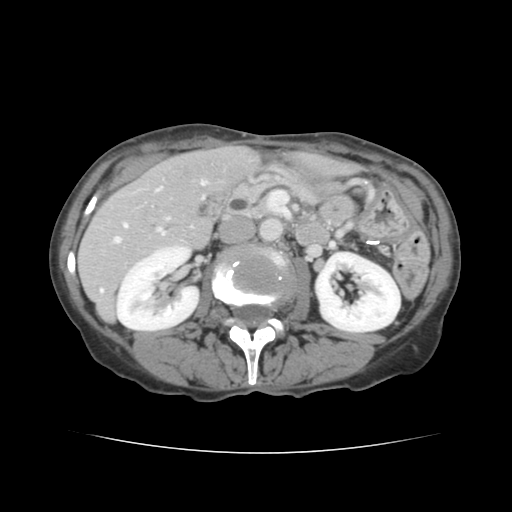
Contrast-enhanced abdominal CT, one axial slice; position 59 of 136 along the scan axis; intravenous contrast given; soft-tissue window (W 400 / L 40 HU); 2.5 mm slice thickness; 512 × 512 image matrix, field of view 319 × 319 mm. Female patient, age 77 years. Case-level facts recorded for this patient, not image findings: diagnosis: colorectal cancer liver metastases, imaged before liver resection.
Outlined on this slice (outlined manually by an expert reader):
- hepatic veins: bounding box <115,181,206,243> (left, top, right, bottom; pixels)
- liver: <79,146,259,319>
- planned liver remnant (the part of the liver to remain after resection): <165,146,259,200>
- portal vein (with intrahepatic branches): <100,228,166,292>